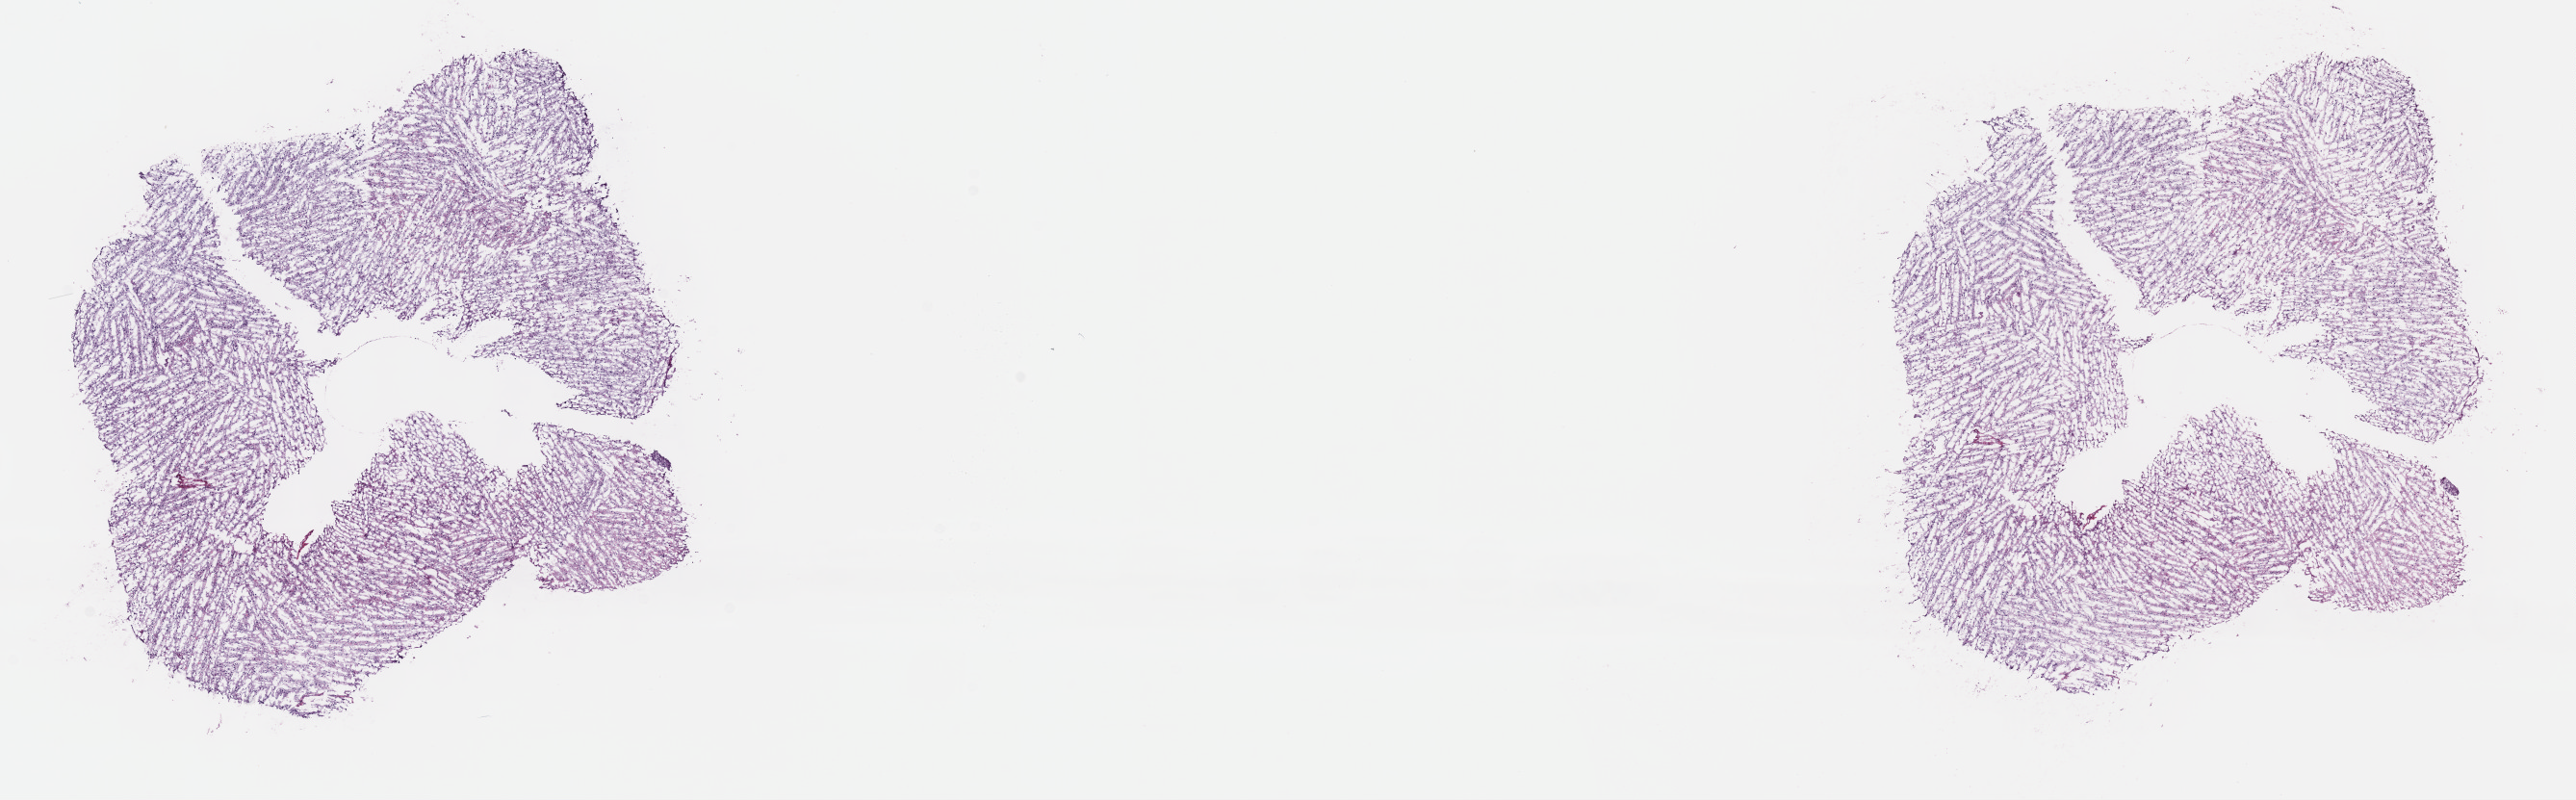
Digitized Hematoxylin and eosin (H&E) stained tissue section (whole slide), shown as a low-resolution overview of the whole scanned area (about 21.6 x 6.7 mm, from a 40x scan), frozen section from the top of the tissue portion, sample: primary tumour, brain. Male, age 49 years at initial diagnosis. Histologic grade: G3 (poorly differentiated). Composition of this section per pathologist review: tumour cells 40%, tumour nuclei 90%, normal cells 10%, stromal cells 50%, necrosis 0%. Inflammatory infiltration, as recorded: lymphocyte infiltration 0%, monocyte infiltration 0%, neutrophil infiltration 0%.
- histologic diagnosis: Astrocytoma, anaplastic